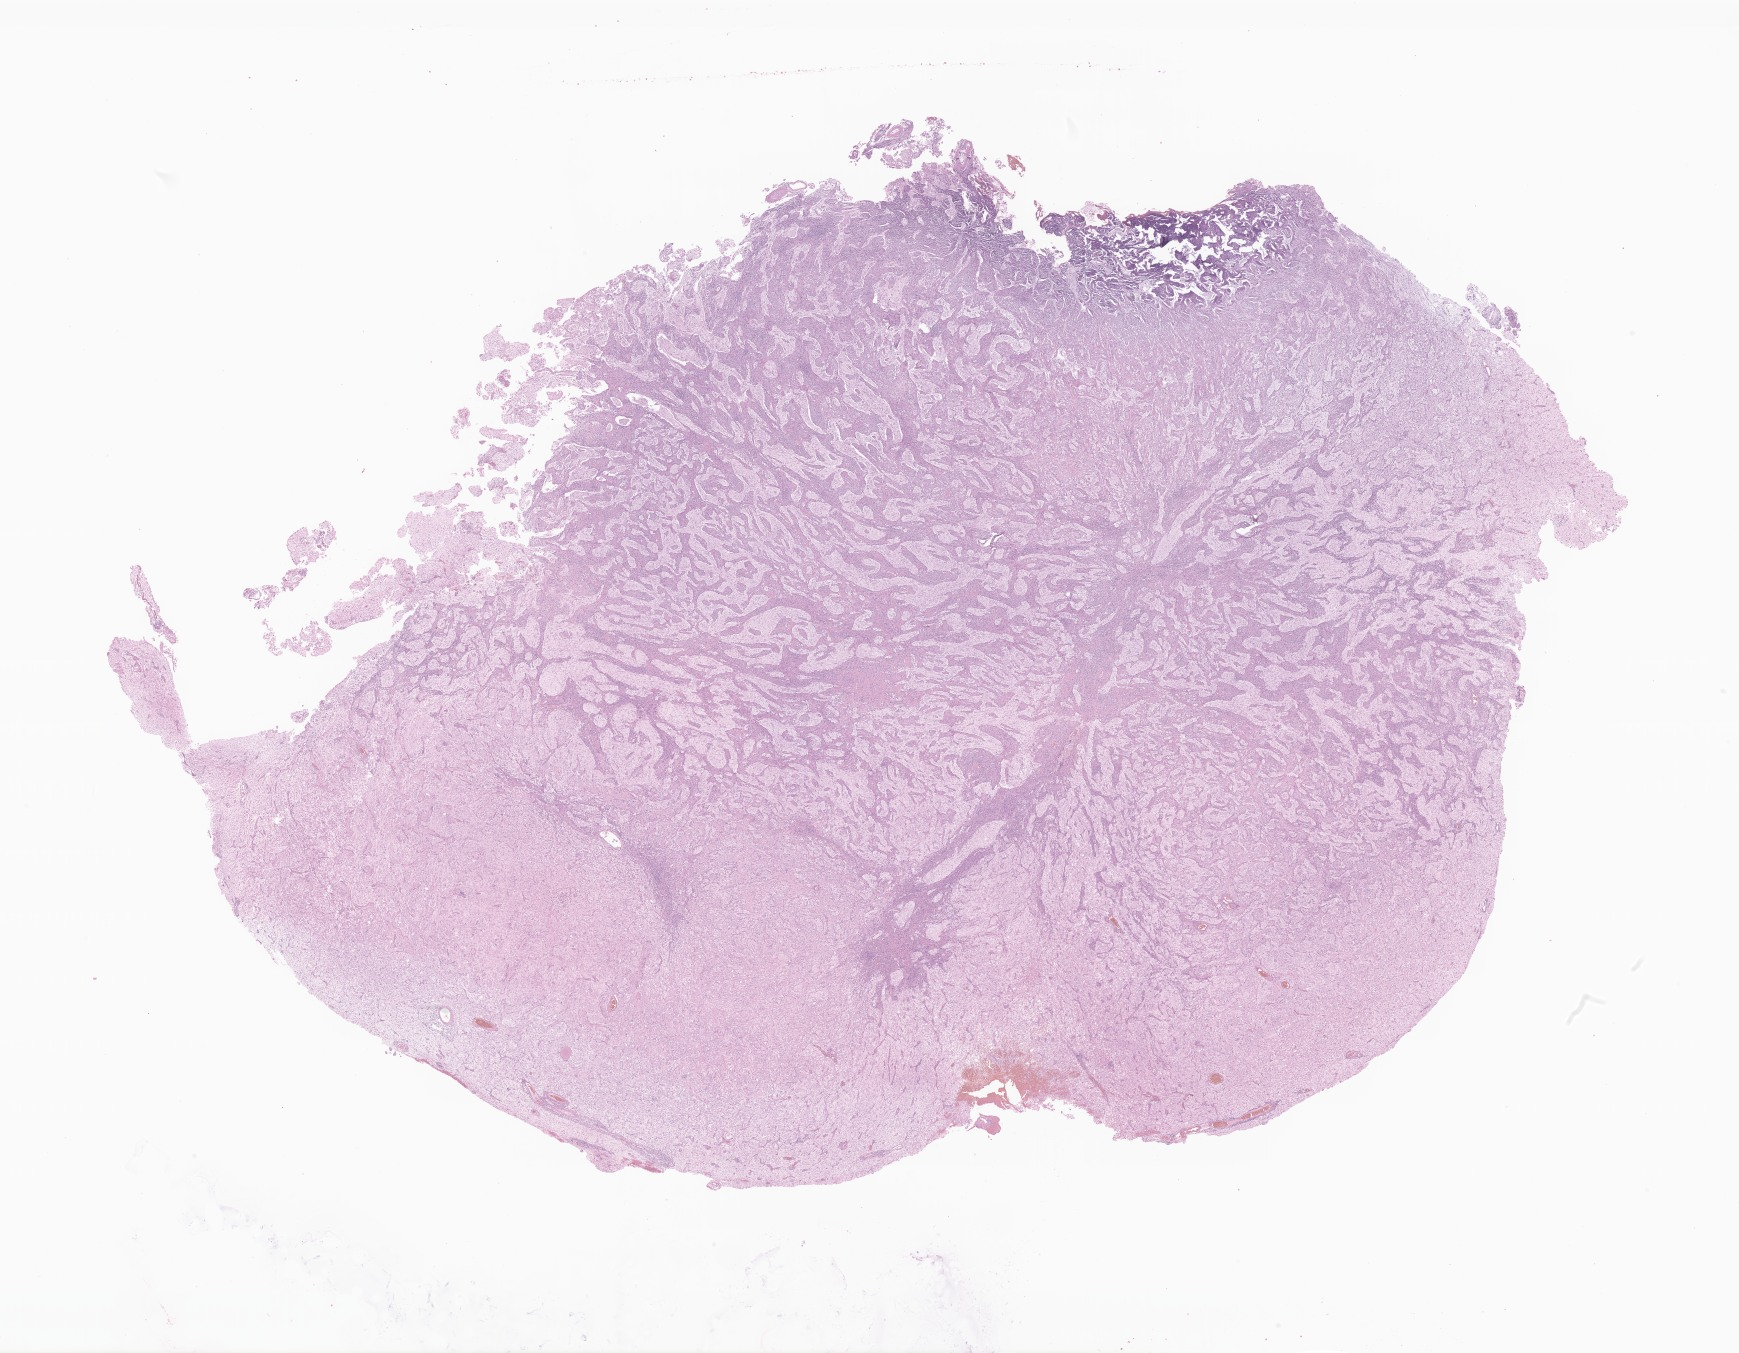
Whole-slide image, hematoxylin and eosin (H&E) stain of tumor tissue from the brain — low-resolution overview of the scanned area, about 29.3 x 22.8 mm, formalin-fixed, paraffin-embedded (FFPE) tissue. Male patient, age 191 months (15 years 11 months).
Diagnosis: Ganglioglioma, NOS.